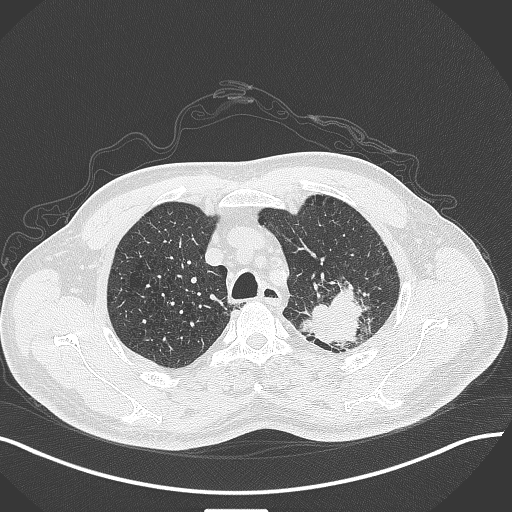
Chest CT, one axial slice; position 338 of 429 along the scan axis; 120 kVp; lung window (W 1500 / L -600 HU); 1 mm slice thickness; 512 × 512 image matrix, field of view 400 × 400 mm. Male patient, age 55 years. From the clinical record (not read from this slice): clinical TNM (as recorded): T3 N0 M1c.
Outlined on this slice (bounding box drawn by a radiologist):
- lung tumour (recorded histology: adenocarcinoma): box from (x=298, y=281) to (x=372, y=346) px